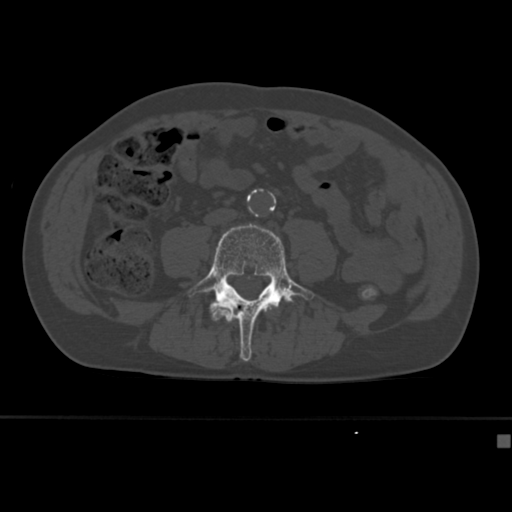
CT including the spine, one axial slice. Position 107 of 430 along the scan axis. Reconstruction kernel Br40s. 120 kVp. Bone window (W 1800 / L 400 HU). 1.5 mm slice thickness. 512 × 512 image matrix, field of view 337 × 337 mm. Patient: male, 64 years. Case-level facts recorded for this patient, not image findings: primary cancer: uterus; vertebrae with lytic lesions (as recorded): T1, T4, T5, T7, L5.
Outlined on this slice (semi-automatic segmentation, software-assisted and operator-edited):
- L4 vertebra: bounding box <189,223,316,362> (left, top, right, bottom; pixels)